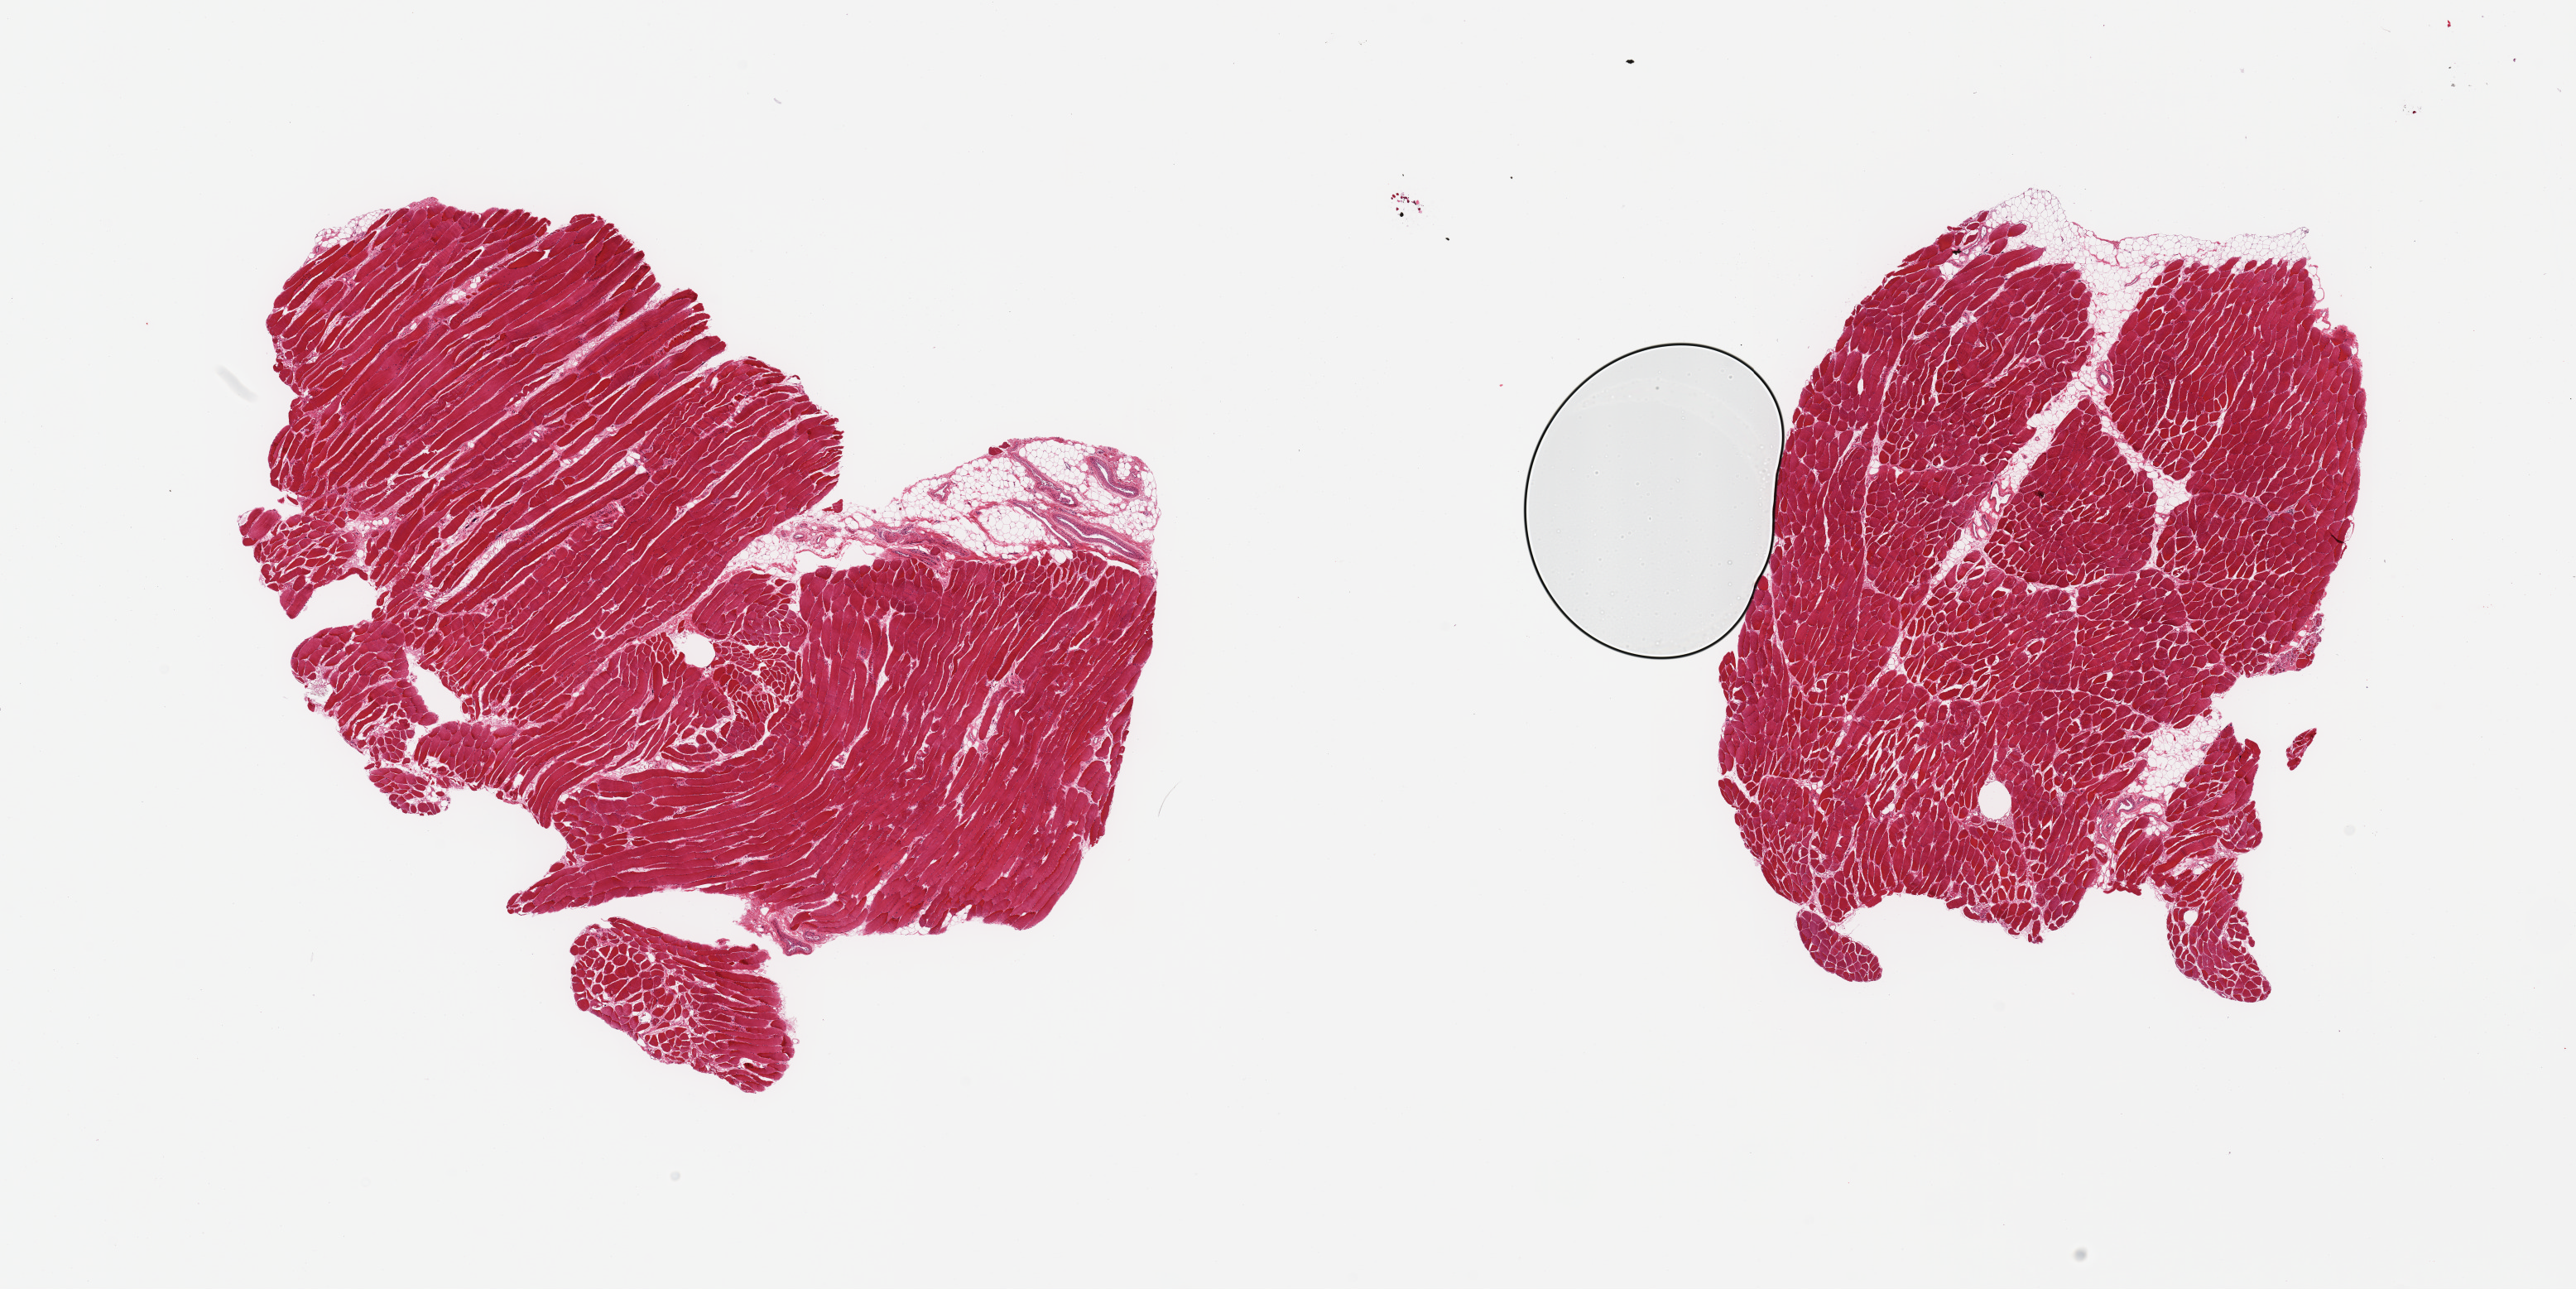
Whole-slide image, H&E stain — whole scanned area (about 24.6 x 12.3 mm) shown as a low-resolution overview, PAXgene-fixed paraffin-embedded (PFPE) section, section of skeletal muscle (target tissue), donor tissue sample. Donor sex: male.
Review note (as recorded): 2 pieces; adherent/interstitial fat/vascular elements ~10%.